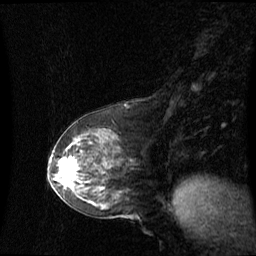
Breast MRI (dynamic contrast-enhanced), one sagittal slice; slice 30 of 60 in the series (ordered by position); dynamic contrast-enhanced series, image 2 of 3 at this slice position (ordered by acquisition); 1.5 T; TE 4.2 ms, TR 8.4 ms; 2.1 mm slice thickness; 256 × 256 image matrix. Female patient, age 59 years. From the clinical record (not read from this slice): setting: breast cancer imaged before/during neoadjuvant chemotherapy; receptor status: HR-positive, HER2-negative.
Annotated regions visible in this slice (semi-automatic segmentation, software-assisted and operator-edited):
- analysis volume of interest (the breast-tissue region the enhancement analysis was run in; not a lesion): bounding box (x1, y1, x2, y2) in pixels: (55, 148, 89, 191)
- tumour enhancement mask (voxels above the 70 % enhancement threshold inside the analysis volume of interest): (61, 160, 78, 173)